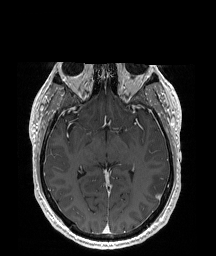
Brain MRI from a brain-tumour surgery series, one axial slice. Slice 109 of 192 in the series (ordered by position). T1-weighted post-contrast. 1 mm slice thickness. 216 × 256 image matrix, field of view 219 × 260 mm. Case-level facts recorded for this patient, not image findings: histopathology: Glioblastoma; WHO grade: 4; IDH mutation: no.
Annotated regions visible in this slice (outlined manually by an expert reader):
- tumour: box from (x=148, y=175) to (x=163, y=198) px